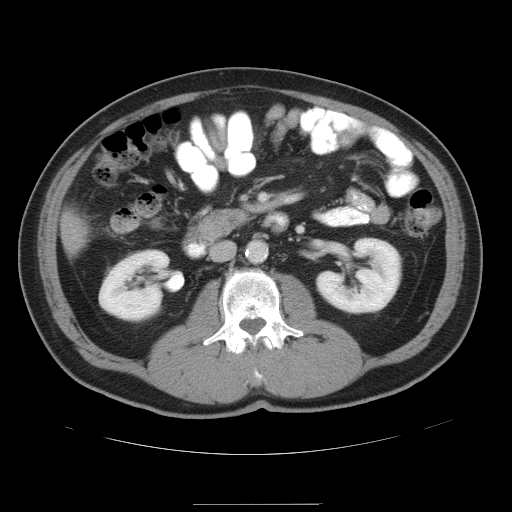
Contrast-enhanced abdominal CT, one axial slice; position 16 of 47 along the scan axis; intravenous contrast given; soft-tissue window (W 400 / L 40 HU); 5 mm slice thickness; 512 × 512 image matrix, field of view 420 × 420 mm. Male patient, age 61 years. From the clinical record (not read from this slice): diagnosis: colorectal cancer liver metastases, imaged before liver resection; multiple liver metastases: no; largest metastasis: 1.2 cm; disease in both lobes: no.
Annotated regions visible in this slice (manually delineated by an expert):
- liver: bounding box [x1, y1, x2, y2] px = [63, 214, 88, 251]